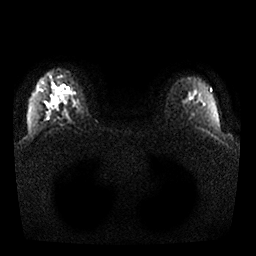
Breast MRI, one axial slice; diffusion-weighted series; image 2 of 4 stored at this slice position (different b-values; order by instance number); 1.5 T; 4 mm slice thickness; 256 × 256 image matrix, field of view 350 × 350 mm. Female patient.
Outlined on this slice (outlined manually by an expert reader):
- tumour on diffusion-weighted imaging: bounding box (x1, y1, x2, y2) in pixels: (50, 98, 56, 107)